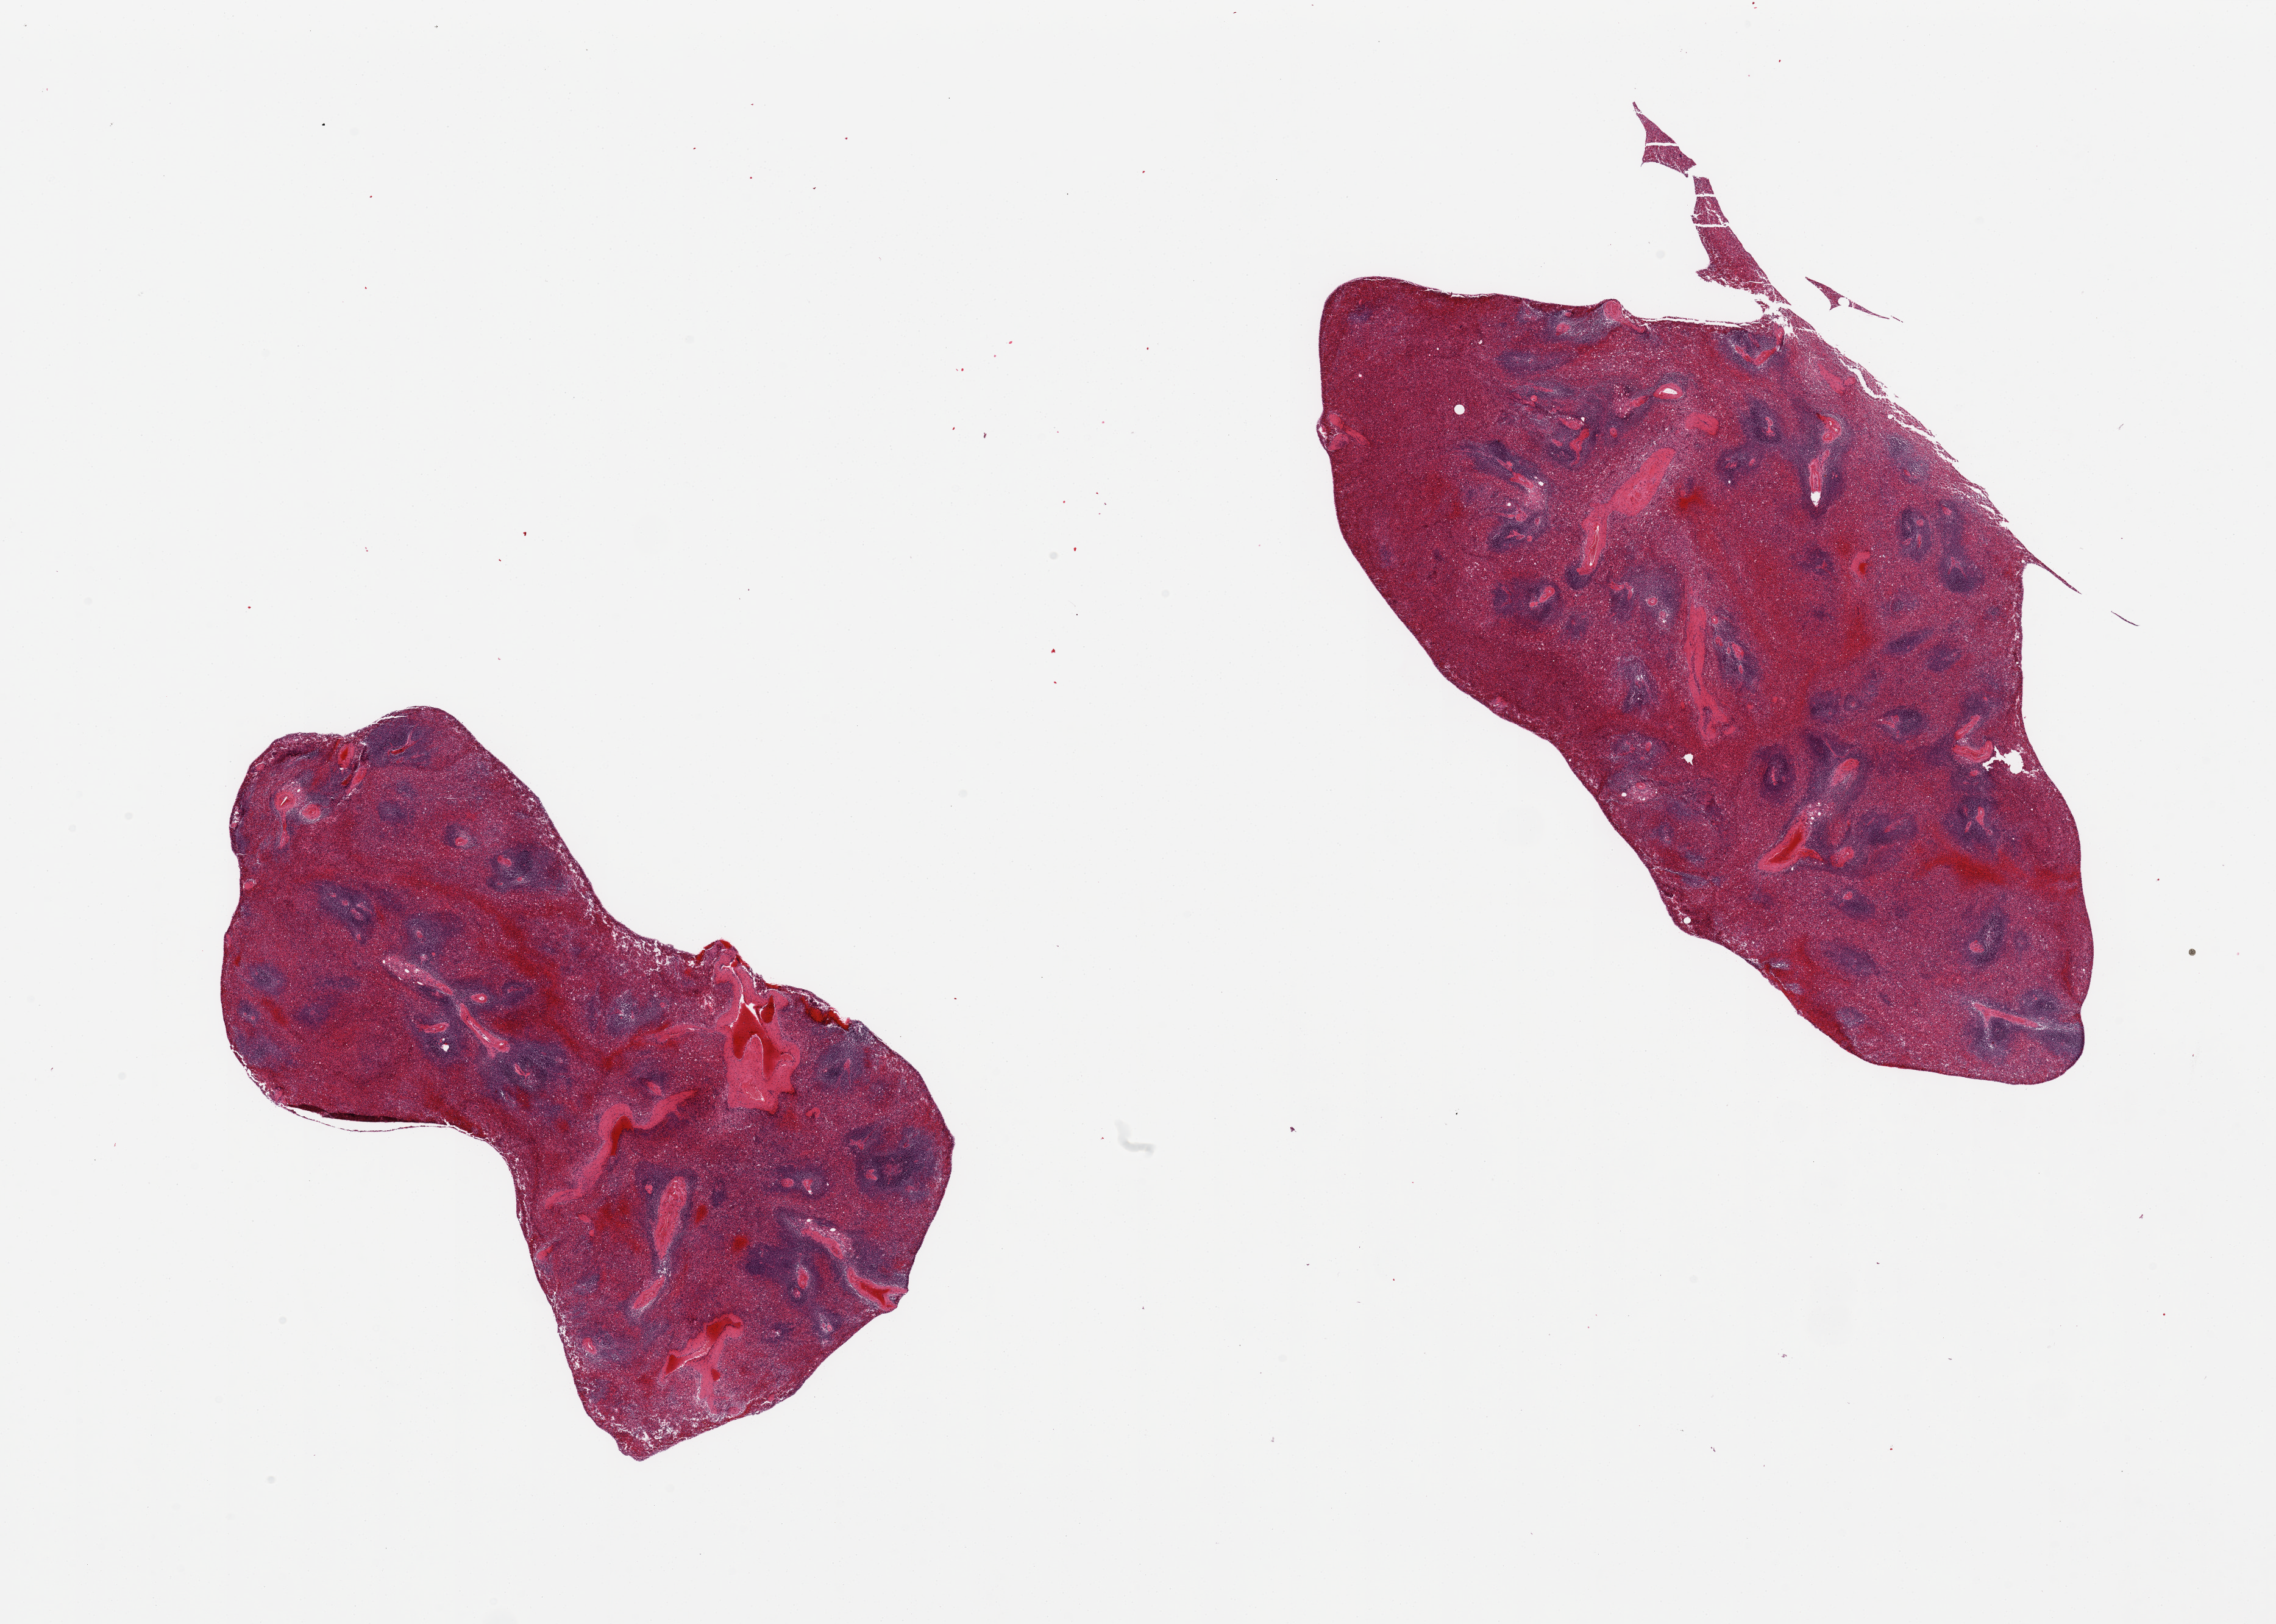
Digitized haematoxylin and eosin-stained section — whole scanned area (about 29.5 x 21.1 mm, slide scanned at 20x) shown as a low-resolution overview. PAXgene-fixed paraffin-embedded (PFPE) section. Target tissue: spleen. Tissue donor sample. Donor sex: male.
Reviewer comment on this tissue sample: 2 pieces, congested.